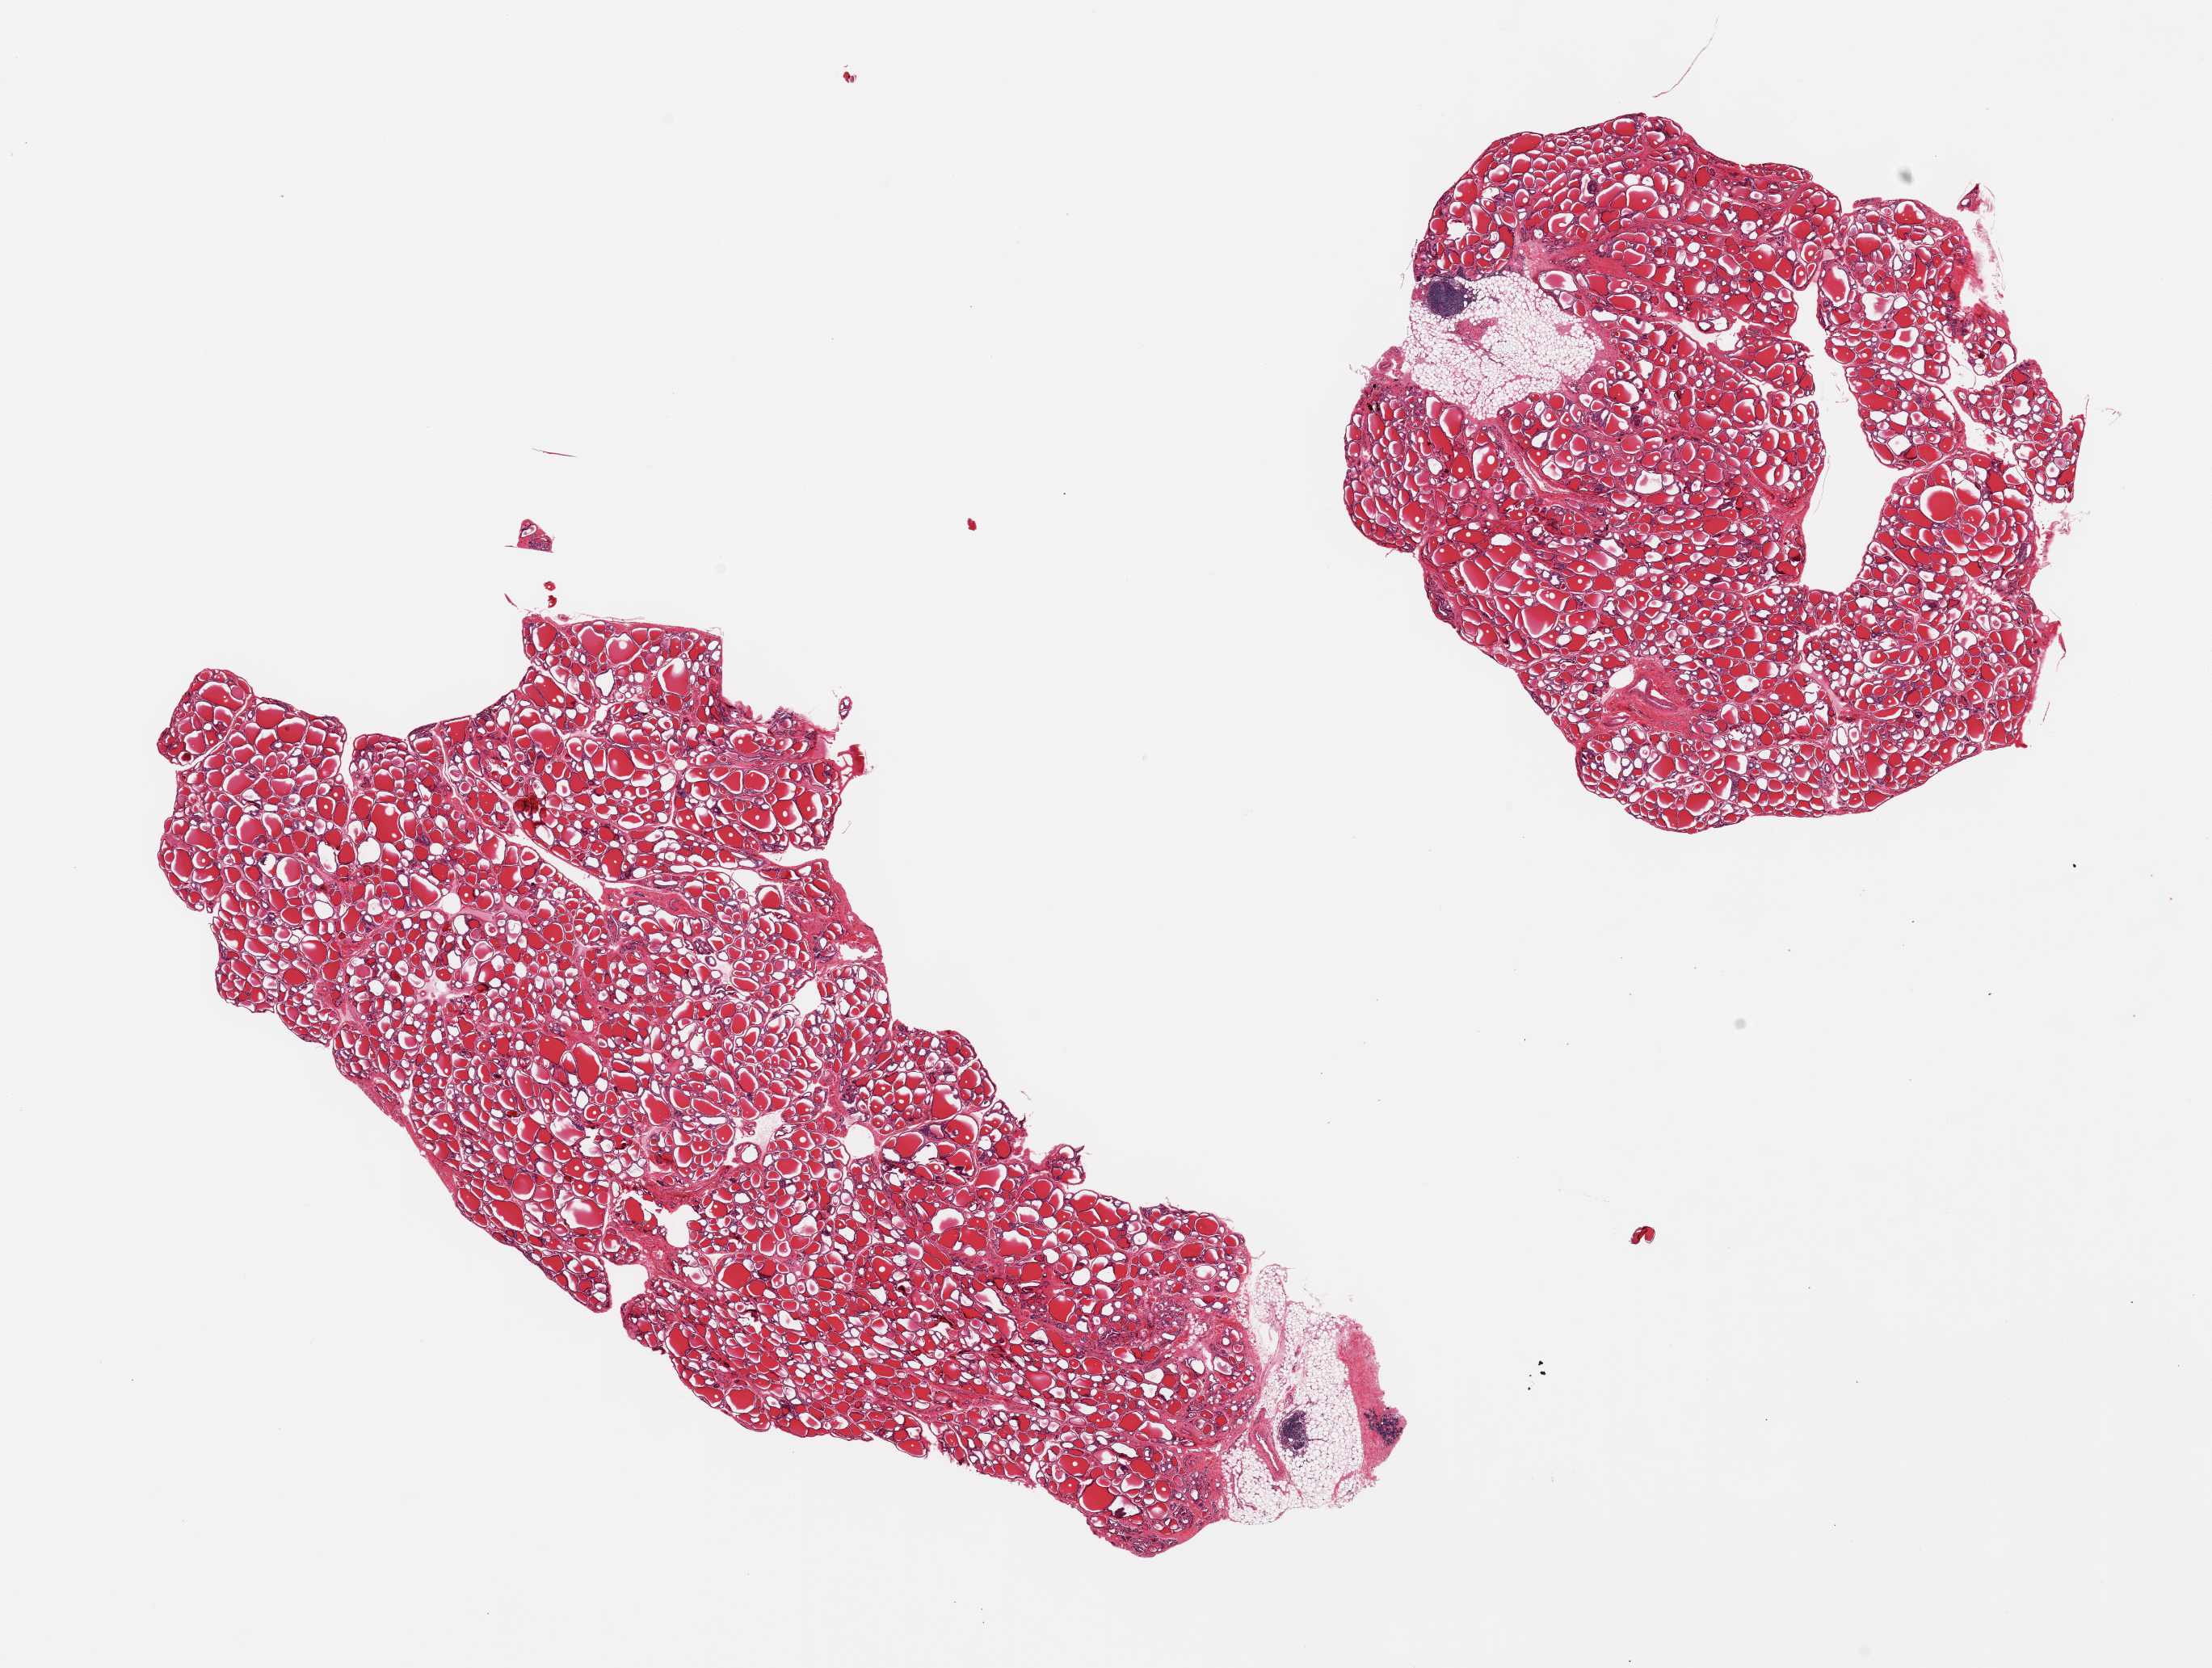
Whole-slide image, haematoxylin and eosin stain, brightfield, a low-resolution overview of the entire scanned area, about 21.7 x 16.3 mm; PAXgene-fixed paraffin-embedded (PFPE) section; target tissue: thyroid; donor tissue sample. Donor: male.
• reviewer comment on this tissue sample: 2 pieces; 10% fat and lymphoid nodule in each at edge